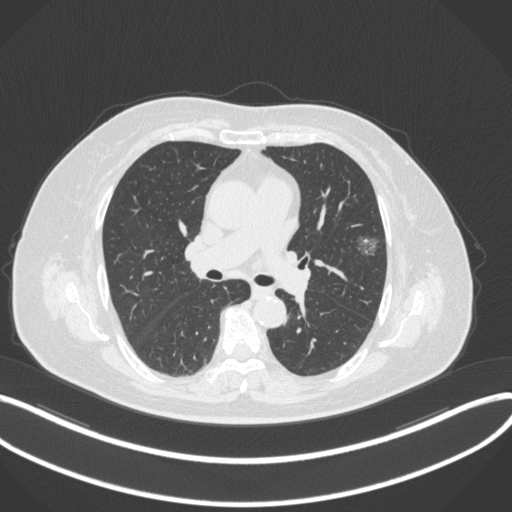
Chest CT, one axial slice. Slice 182 of 286 in the series (ordered by position). Lung window (W 1500 / L -600 HU). 1 mm slice thickness. 512 × 512 image matrix, field of view 400 × 400 mm. Patient: female, 76 years. From the clinical record (not read from this slice): clinical TNM (as recorded): T1b N0 M0.
Outlined on this slice (bounding box drawn by a radiologist):
- lung tumour (recorded histology: adenocarcinoma): bounding box [x1, y1, x2, y2] px = [353, 229, 386, 264]